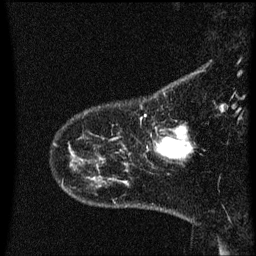
Breast MRI (dynamic contrast-enhanced), one sagittal slice. Position 8 of 60 along the scan axis. Dynamic contrast-enhanced series, image 2 of 3 at this slice position (ordered by acquisition). 1.5 T. TE 4.2 ms, TR 8.4 ms. 256 × 256 image matrix, field of view 200 × 200 mm. Patient: female, 41 years. From the clinical record (not read from this slice): setting: breast cancer imaged before/during neoadjuvant chemotherapy; receptor status: triple-negative.
Structures marked on this image (semi-automatically segmented with operator editing):
- analysis volume of interest (the breast-tissue region the enhancement analysis was run in; not a lesion): bounding box <146,128,189,159> (left, top, right, bottom; pixels)
- tumour enhancement mask (voxels above the 70 % enhancement threshold inside the analysis volume of interest): <160,128,189,157>